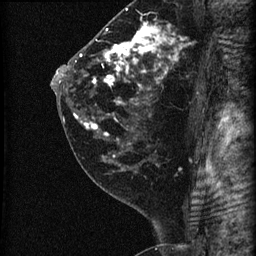
Breast MRI (dynamic contrast-enhanced), one sagittal slice; slice 39 of 60 in the series (ordered by position); dynamic contrast-enhanced series, image 2 of 3 at this slice position (ordered by acquisition); 1.5 T; TE 4.2 ms, TR 22.7 ms; 1.8 mm slice thickness; 256 × 256 image matrix, field of view 180 × 180 mm. Patient: female, 45 years. Case-level facts recorded for this patient, not image findings: setting: breast cancer imaged before/during neoadjuvant chemotherapy; receptor status: HR-positive, HER2-negative.
Annotated regions visible in this slice (semi-automatic segmentation, software-assisted and operator-edited):
- analysis volume of interest (the breast-tissue region the enhancement analysis was run in; not a lesion): box from (x=74, y=11) to (x=205, y=140) px
- tumour enhancement mask (voxels above the 90 % enhancement threshold inside the analysis volume of interest): (x=75, y=23)–(x=182, y=135)